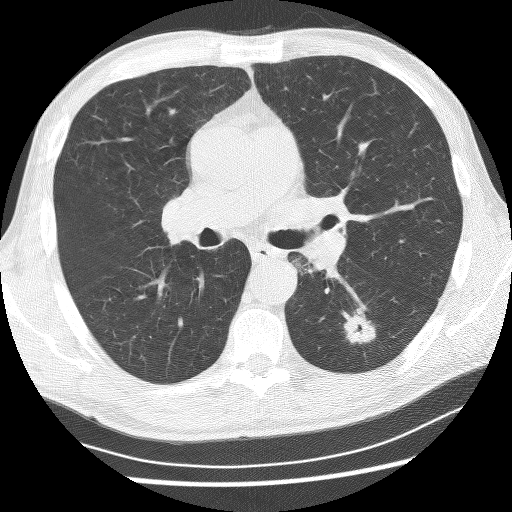
Low-dose screening chest CT, axial slice. First (baseline) screen. Lung window (W 1500 / L -600 HU). 2.5 mm slice thickness. Lung (sharp) reconstruction kernel (BONE). 120 kVp. Slice 108 of 253 in the series. 512 × 512 image matrix, field of view 340 × 340 mm. Male participant, aged 62 years at enrolment. Current smoker at enrolment.
Lesion marked by an expert reader, bounding box [x1, y1, x2, y2] px = [330, 307, 382, 352]. The exam's reader record, not a measurement of the box and not confirmed to be the same lesion: non-calcified nodule or mass ≥4 mm, left lower lobe, 21 × 17 mm, spiculated (stellate) margins, soft tissue attenuation. Participant outcome: lung cancer diagnosed 58 days after this screen — non-small cell carcinoma, left lower lobe, poorly differentiated (G3), stage IA (AJCC 6th edition), 11 mm at pathology.